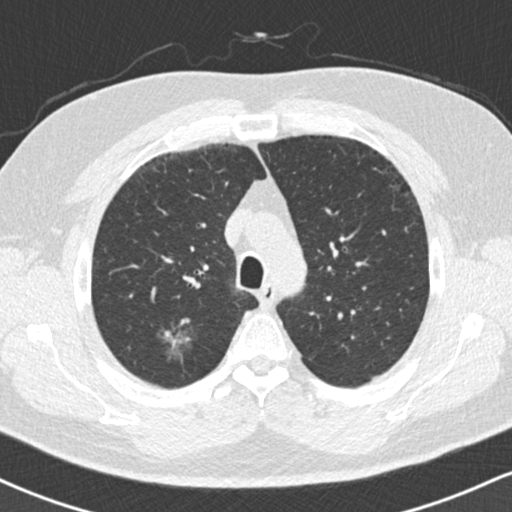
Low-dose screening chest CT, axial slice. Second screening round (one year after baseline). Lung window (W 1500 / L -600 HU). 512 × 512 image matrix. Male, age 59 years at enrolment. Current smoker at enrolment.
Expert reader's lesion annotation, bounding box (x1, y1, x2, y2) in pixels: (152, 306, 206, 362). Screening reader's record for this exam (one nodule recorded; not confirmed to be the boxed lesion): non-calcified nodule or mass ≥4 mm, right upper lobe, 18 × 16 mm, ground glass attenuation, pre-existing on the prior screen: yes. Official screen result: positive, no significant change: stable abnormalities potentially related to lung cancer, unchanged since the prior screening exam.